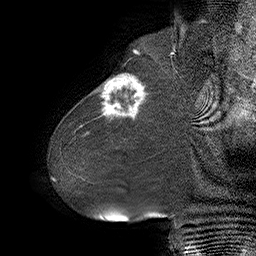
Breast MRI (dynamic contrast-enhanced), one sagittal slice; position 13 of 55 along the scan axis; dynamic contrast-enhanced series, time point 2 of 6 at this slice position (early post-contrast); 1.5 T; TE 4.5 ms, TR 32.4 ms; 3 mm slice thickness; 256 × 256 image matrix, field of view 180 × 180 mm. Female patient. From the clinical record (not read from this slice): setting: breast cancer imaged before/during neoadjuvant chemotherapy; receptor status: HER2-positive.
Outlined on this slice (semi-automatically segmented with operator editing):
- analysis volume of interest (the breast-tissue region the enhancement analysis was run in; not a lesion): bounding box (x1, y1, x2, y2) in pixels: (80, 64, 163, 134)
- tumour enhancement mask (voxels above the 100 % enhancement threshold inside the analysis volume of interest): (100, 75, 146, 118)